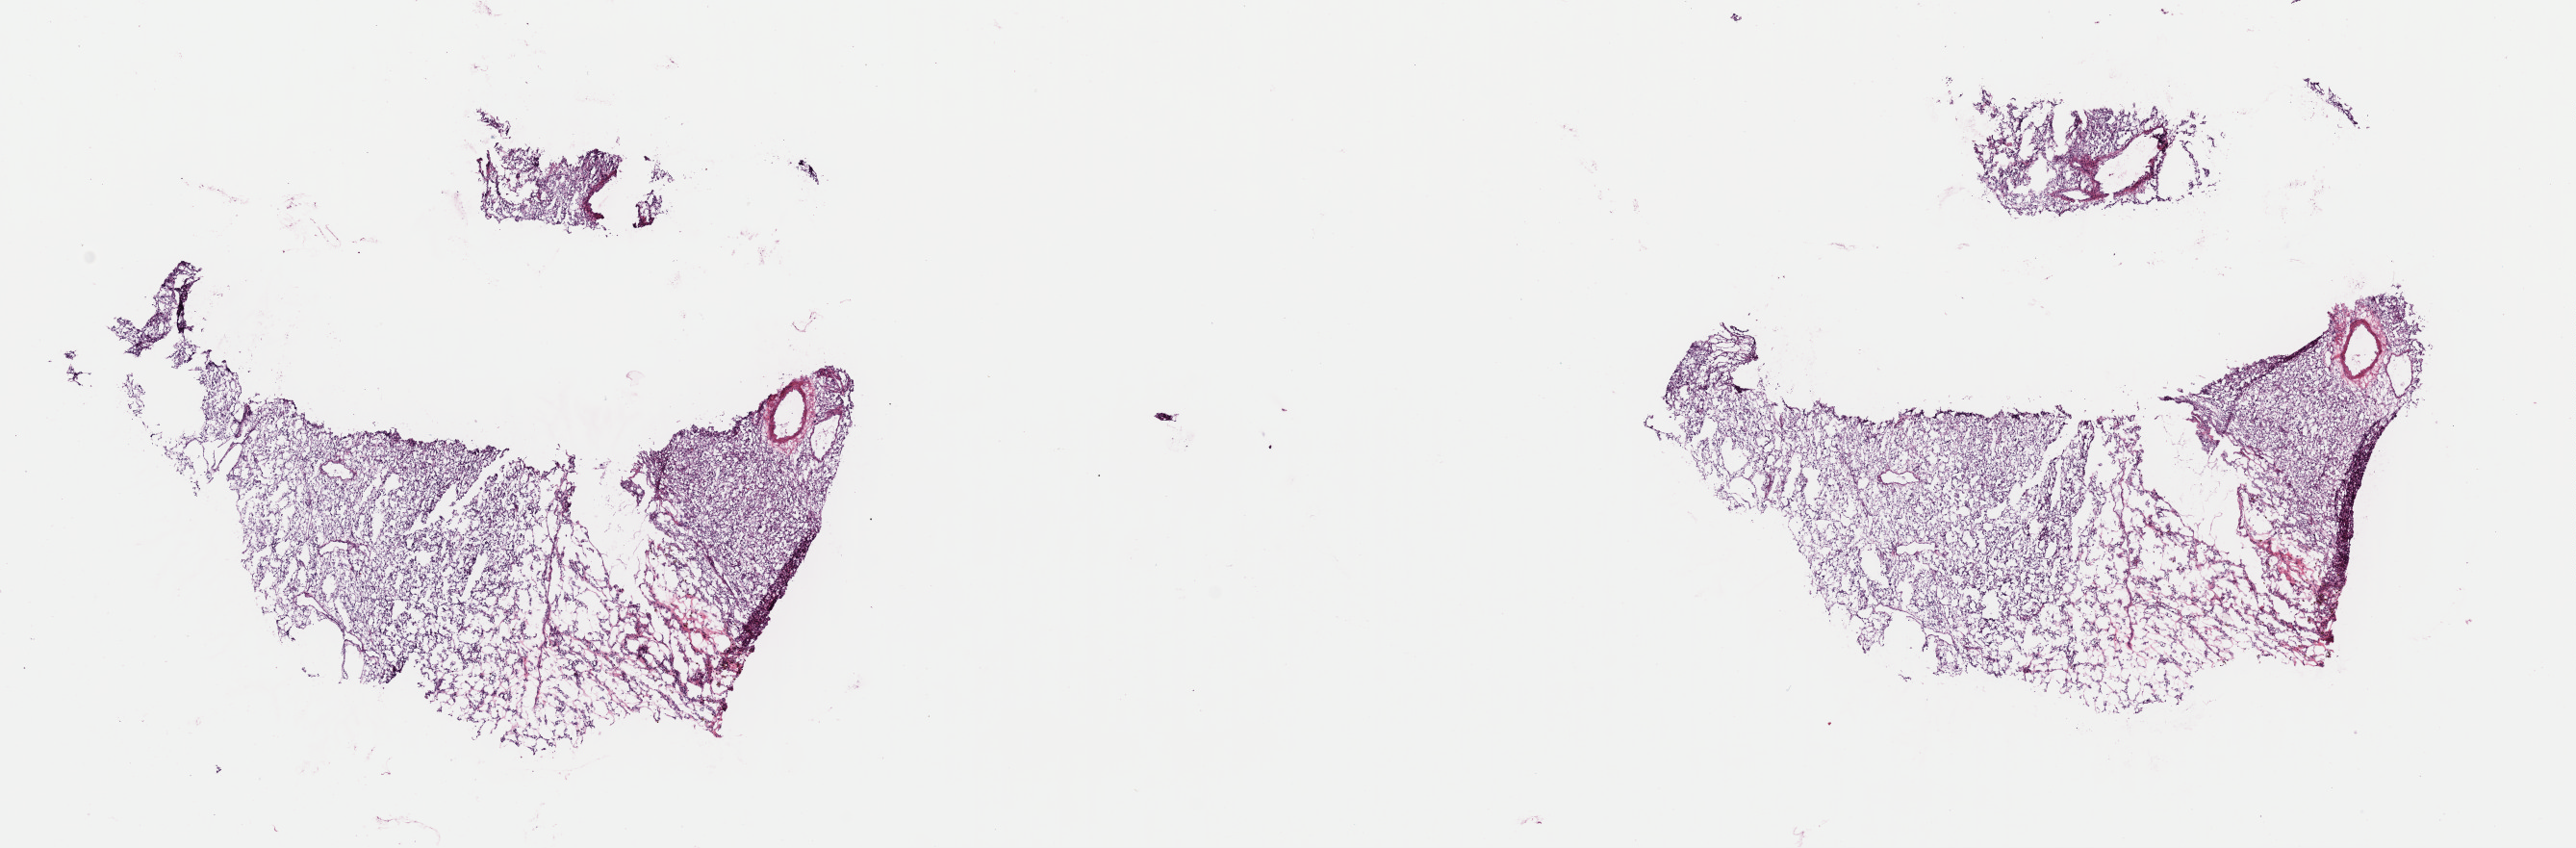
Digitized H&E tissue section (whole slide) — low-resolution overview of the scanned area, about 21.1 x 7.0 mm, frozen section from the top of the tissue portion, kidney, primary tumour sample. Female, age 57 years at initial diagnosis. Histologic grade: G1 (well differentiated). Composition of this section per pathologist review: tumour cells 85%, tumour nuclei 85%, normal cells 0%, stromal cells 15%, necrosis 0%. Infiltration values recorded for this section: lymphocyte infiltration 2%, monocyte infiltration 0%, neutrophil infiltration 0%.
• AJCC pathologic stage: I (7th edition)
• pathologic diagnosis: Renal cell carcinoma, NOS
• TNM: T1a NX MX
• laterality: left